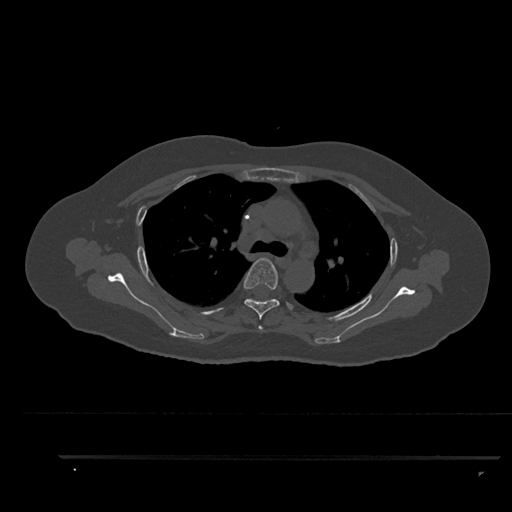
CT including the spine, one axial slice; position 639 of 797 along the scan axis; reconstruction kernel Br40s/3; 120 kVp; bone window (W 1800 / L 400 HU); 0.5 mm slice thickness; 512 × 512 image matrix, field of view 408 × 408 mm. Patient: female, 44 years. From the clinical record (not read from this slice): primary cancer: renal; vertebrae with lytic lesions (as recorded): L1.
Annotated regions visible in this slice (semi-automatically segmented with operator editing):
- T3 vertebra: bounding box <258,325,263,331> (left, top, right, bottom; pixels)
- T4 vertebra: <243,258,293,320>
- T5 vertebra: <245,299,247,301>